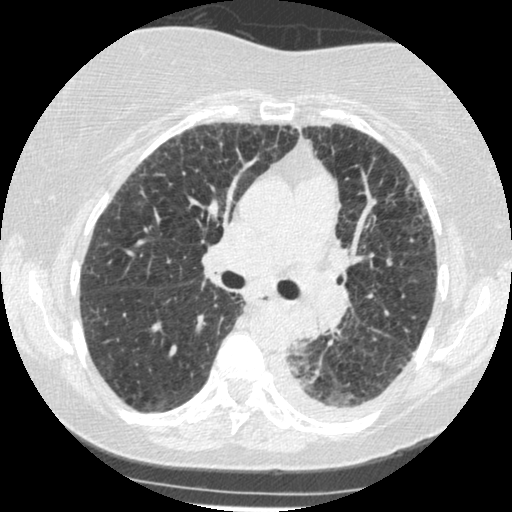
Low-dose screening chest CT, one axial slice. Slice 160 of 341 in the series (ordered by position). Reconstruction kernel STANDARD. 120 kVp. Lung window (W 1500 / L -600 HU). 1.25 mm slice thickness. 512 × 512 image matrix, field of view 310 × 310 mm.
Structures marked on this image (manually delineated by an expert):
- lesion 1 (tumor, lower lobe of left lung): box from (x=293, y=306) to (x=320, y=341) px